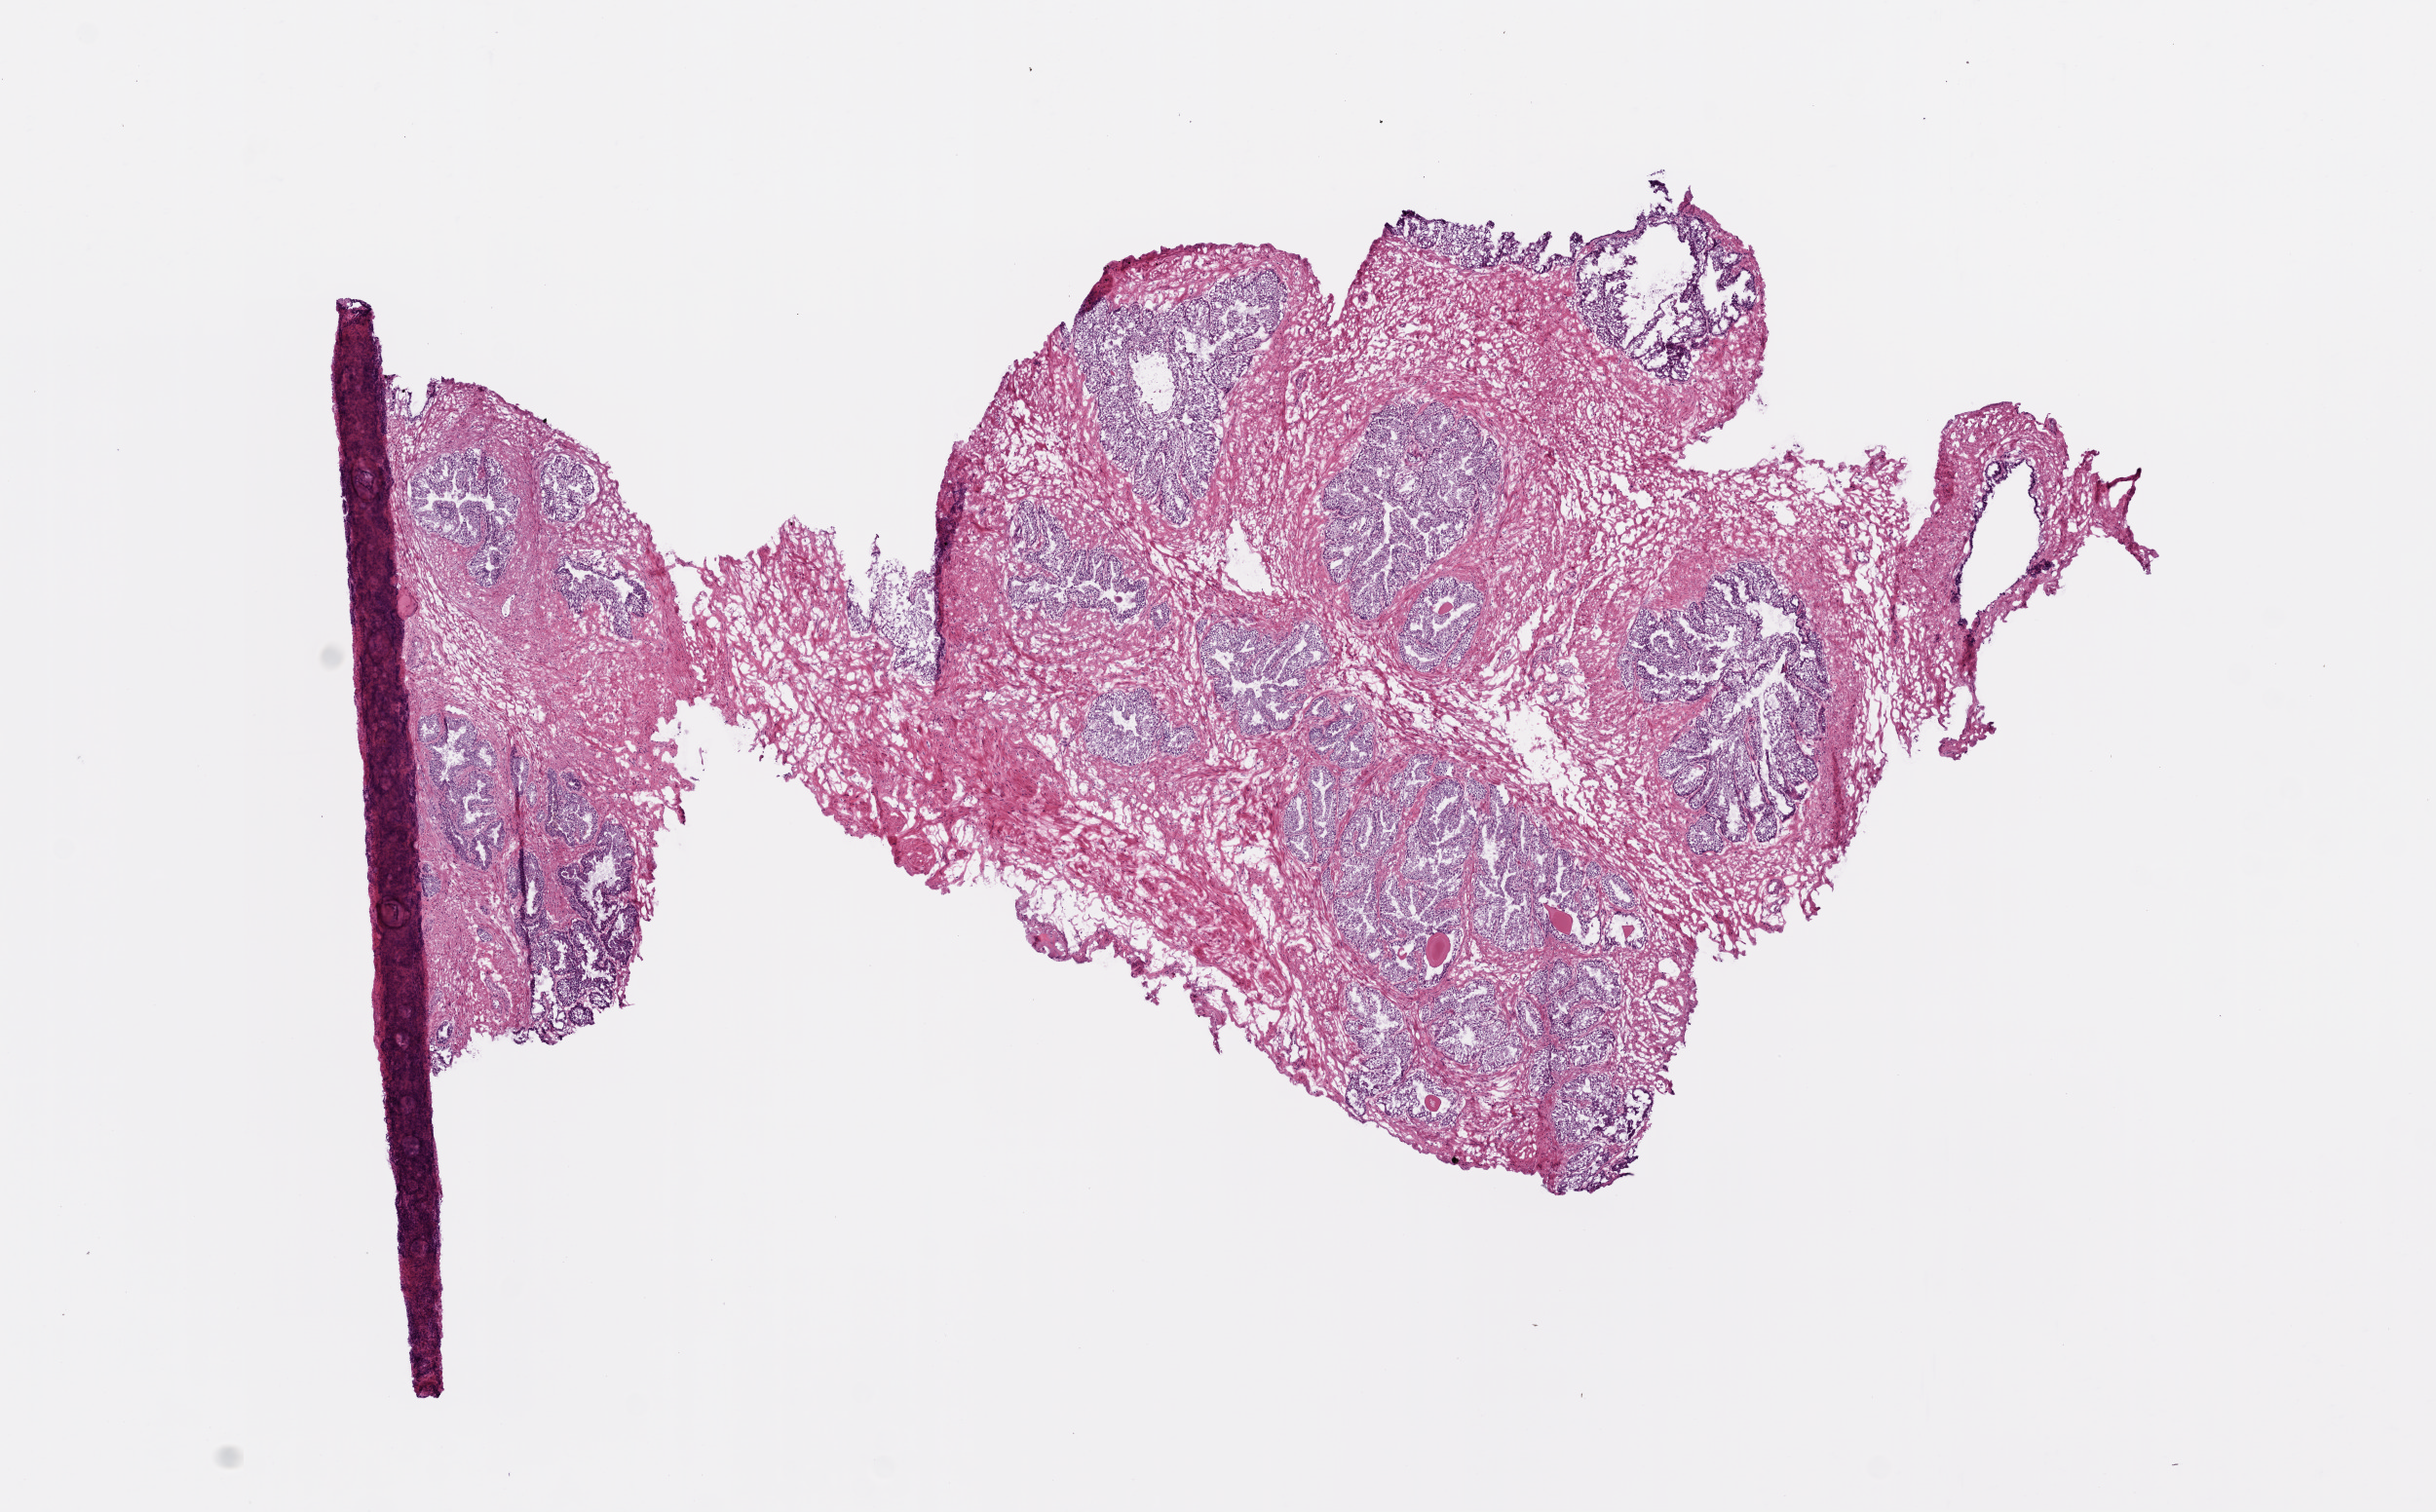
Whole-slide histology image, H&E-stained, whole scanned area (about 10.0 x 6.2 mm) shown as a low-resolution overview; frozen section from the top of the tissue portion; solid tissue normal (non-tumour tissue) sample from the prostate. Male, age 72 years at initial diagnosis.
This section: solid tissue normal (non-tumour) sample from the same patient. Patient diagnosis: Acinar cell carcinoma.